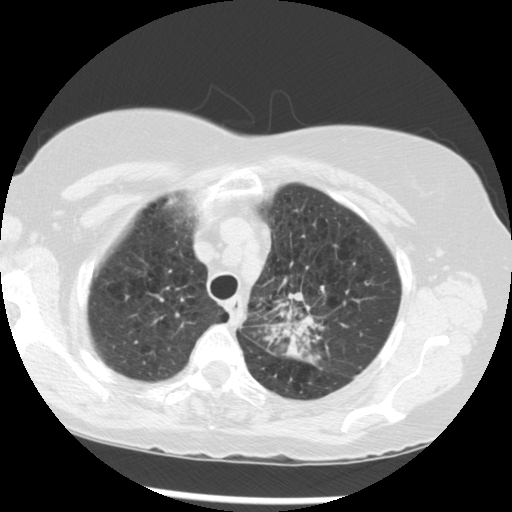
Low-dose screening chest CT, one axial slice; lung window (W 1500 / L -600 HU); 2.5 mm slice thickness; 512 × 512 image matrix, field of view 330 × 330 mm.
Annotated regions visible in this slice (manually delineated by an expert):
- lesion 1 (tumor, upper lobe of left lung): bounding box <278,291,323,363> (left, top, right, bottom; pixels)